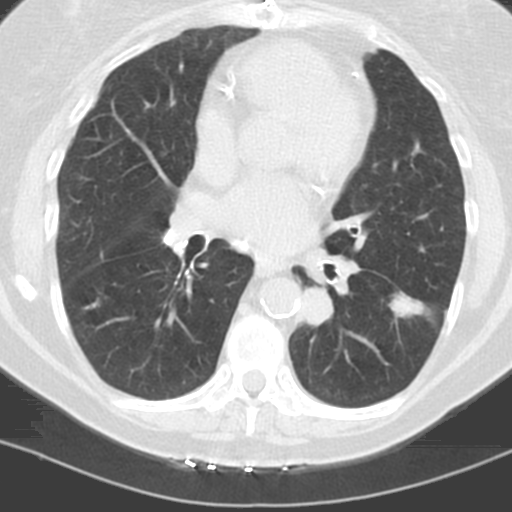
Low-dose screening chest CT, one axial slice; slice 55 of 121 in the series (ordered by position); lung window (W 1500 / L -600 HU); 3.2 mm slice thickness; 512 × 512 image matrix.
Structures marked on this image (expert manual segmentation):
- lesion 1 (tumor, lower lobe of left lung): bounding box [x1, y1, x2, y2] px = [391, 294, 423, 317]
- lesion 2 (tumor, lower lobe of left lung): [303, 287, 333, 326]